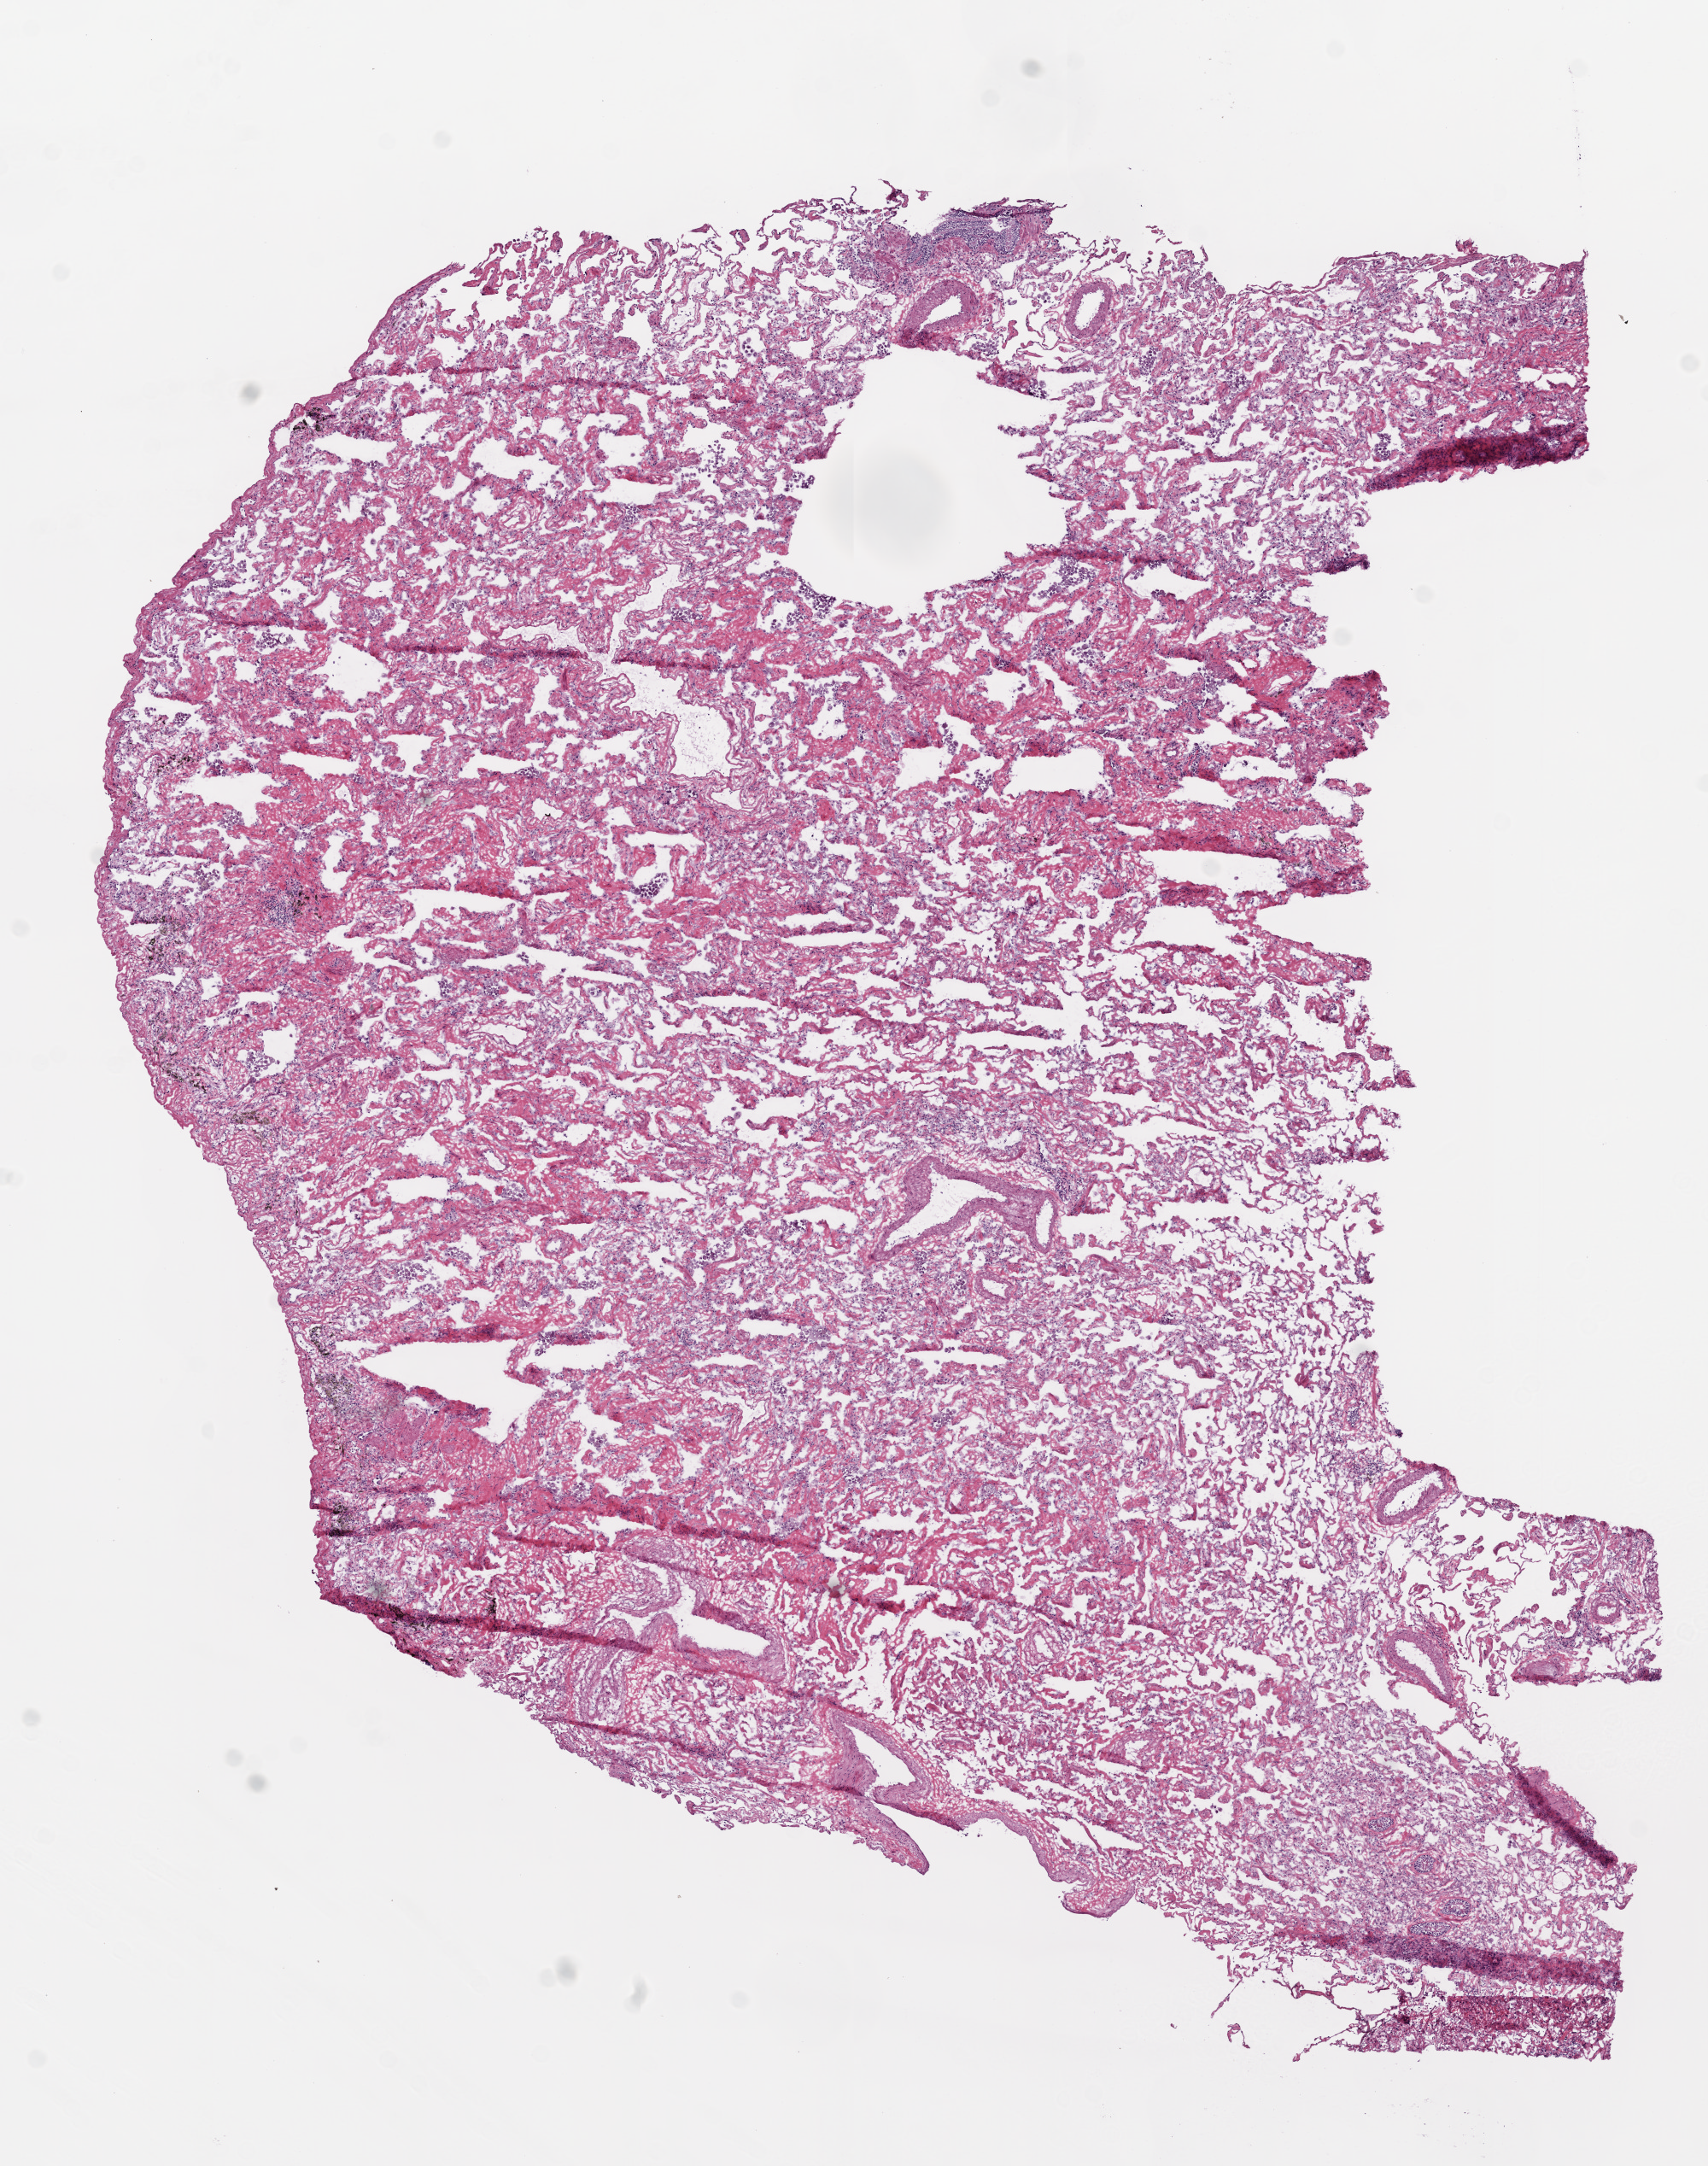
Digitized H&E-stained tissue section (whole slide) — whole scanned area (about 8.0 x 10.2 mm, acquisition: 20x scan) shown as a low-resolution overview. Frozen section. Lung, solid tissue normal (non-tumour tissue) sample. Female patient; age at initial diagnosis 73 years.
* this section: solid tissue normal (non-tumour) sample from the same patient
* patient diagnosis: Squamous cell carcinoma, NOS (upper lobe, lung)